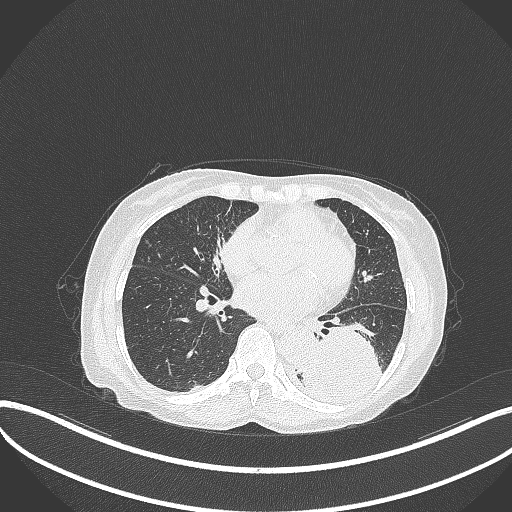
Chest CT, one axial slice; slice 135 of 370 in the series (ordered by position); reconstruction kernel B70f; lung window (W 1500 / L -600 HU); 512 × 512 image matrix. Female patient, age 78 years. From the clinical record (not read from this slice): clinical TNM (as recorded): T3 N0 M1.
Outlined on this slice (bounding box drawn by a radiologist):
- lung tumour (recorded histology: squamous cell carcinoma): bounding box <303,324,387,406> (left, top, right, bottom; pixels)